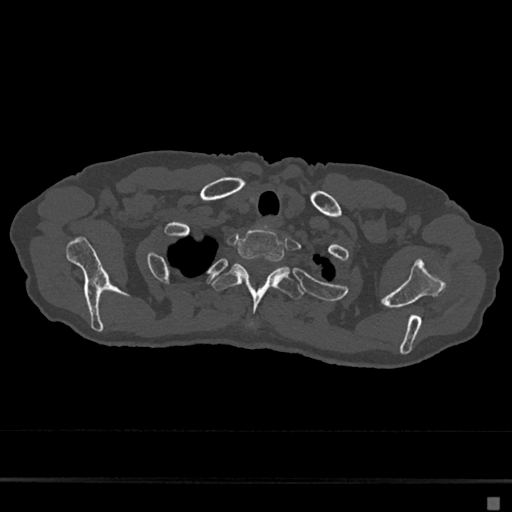
CT including the spine, one axial slice; slice 590 of 797 in the series (ordered by position); reconstruction kernel Br40s/3; bone window (W 1800 / L 400 HU); 512 × 512 image matrix, field of view 360 × 360 mm. Patient: female, 68 years. From the clinical record (not read from this slice): primary cancer: renal.
Annotated regions visible in this slice (semi-automatically segmented with operator editing):
- T1 vertebra: bounding box [x1, y1, x2, y2] px = [237, 227, 285, 262]
- T2 vertebra: [212, 263, 304, 326]